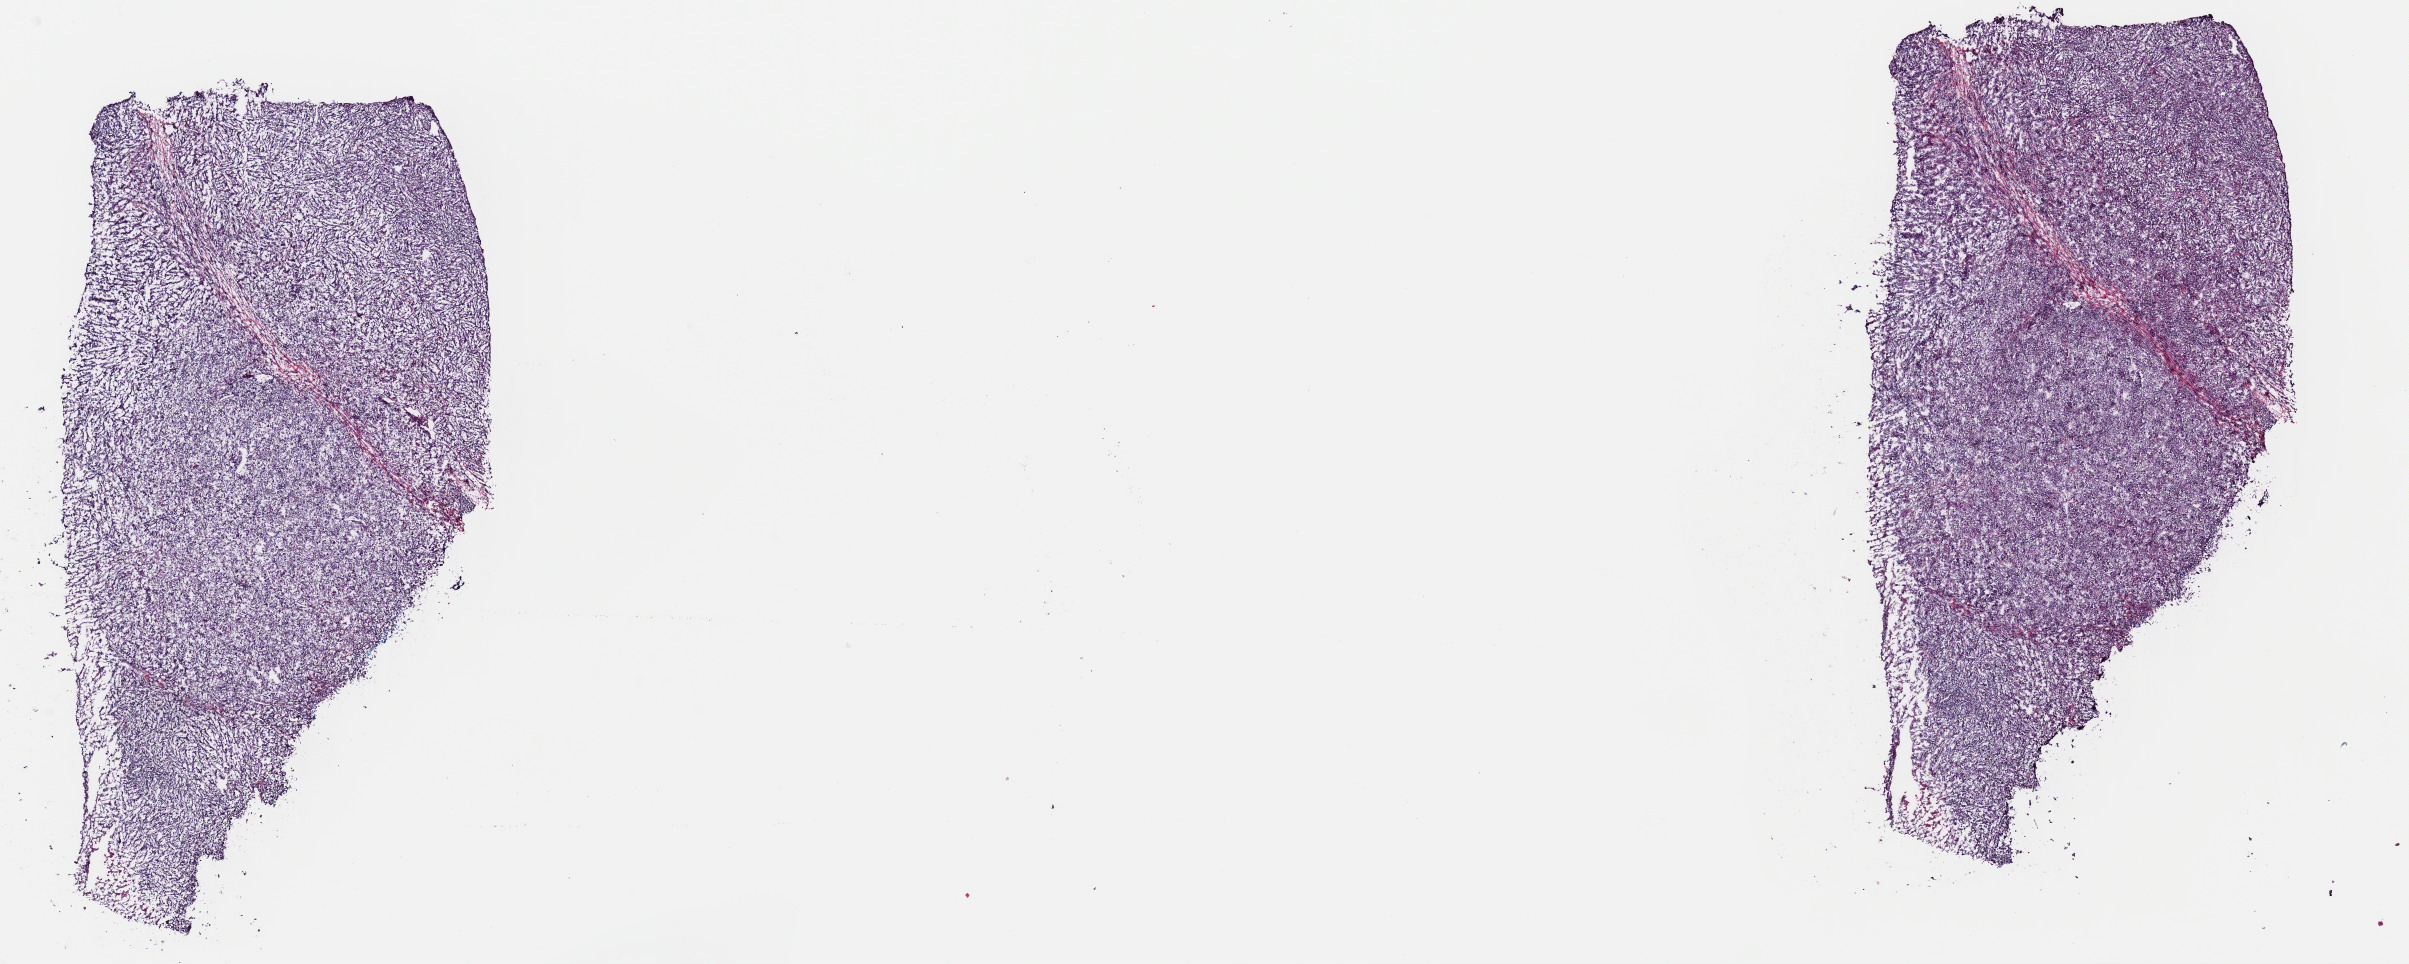
Whole-slide histology image, H&E, low-resolution overview of the scanned area, about 19.0 x 7.6 mm (from a 40x scan); frozen section; metastatic tumour sample, sampled site: lymph nodes of axilla or arm. Male, age 66 years at initial diagnosis. Slide review estimates, as recorded: tumour cells 100%, tumour nuclei 80%, normal cells 0%, stromal cells 0%, necrosis 0%. Infiltration values recorded for this section: lymphocyte infiltration 10%, monocyte infiltration 0%, neutrophil infiltration 0%.
- this section: metastatic tumour tissue
- patient diagnosis: Malignant melanoma, NOS